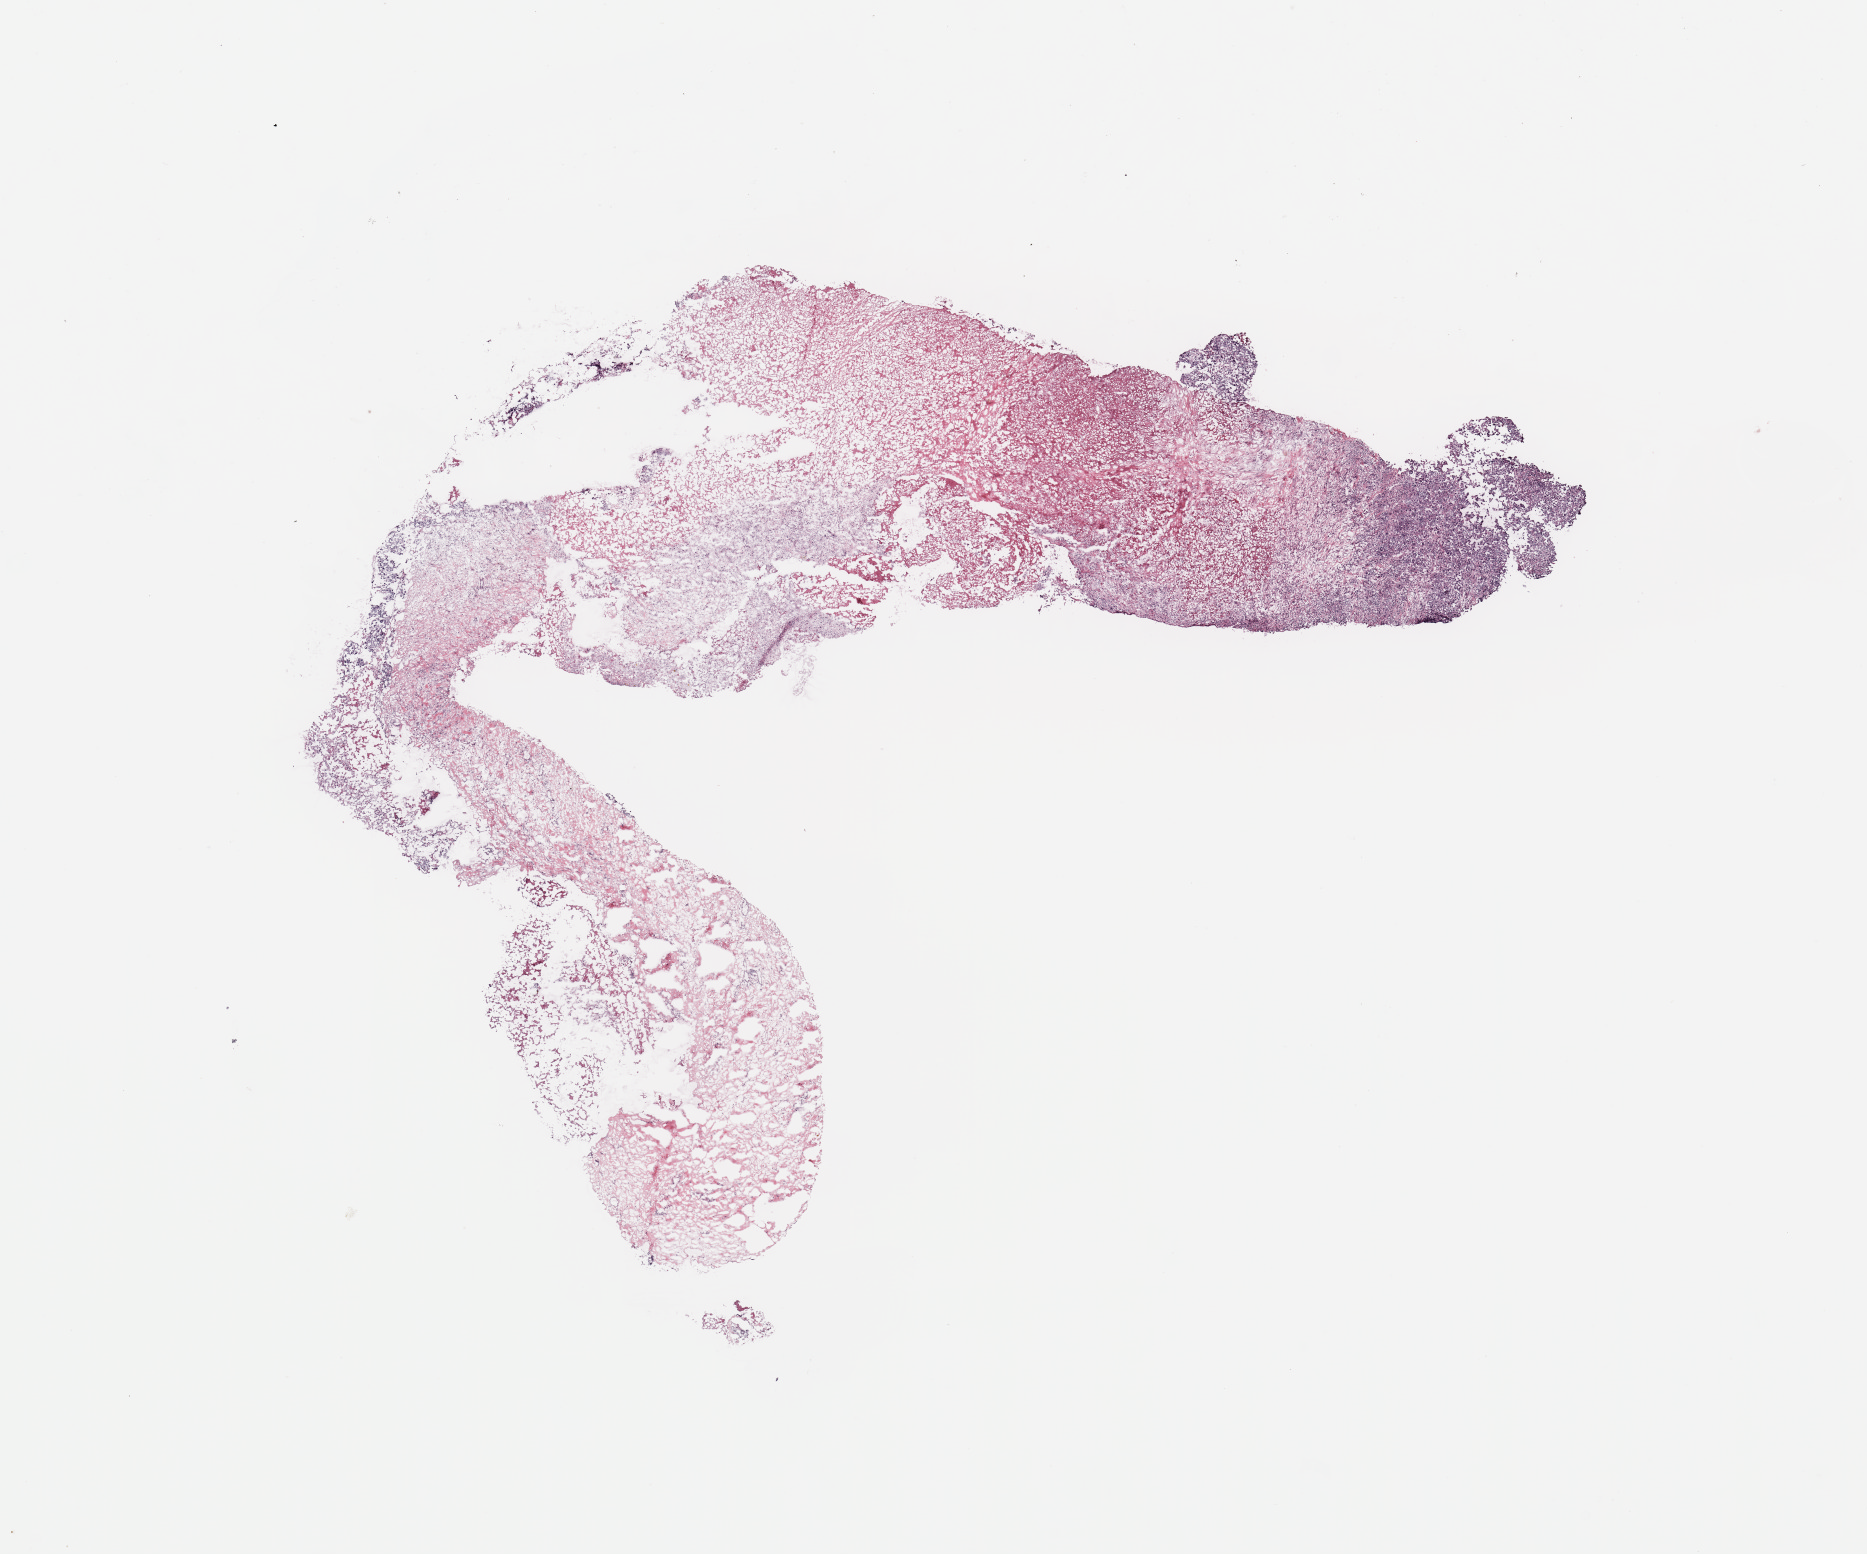
Hematoxylin and eosin (H&E) stained whole-slide image, shown as a low-resolution overview of the whole scanned area (about 14.8 x 12.3 mm, acquisition: 20x scan), tumour tissue sample, breast. 58-year-old female patient.
AJCC pathologic stage: II. Histologic diagnosis: Infiltrating duct carcinoma, NOS.